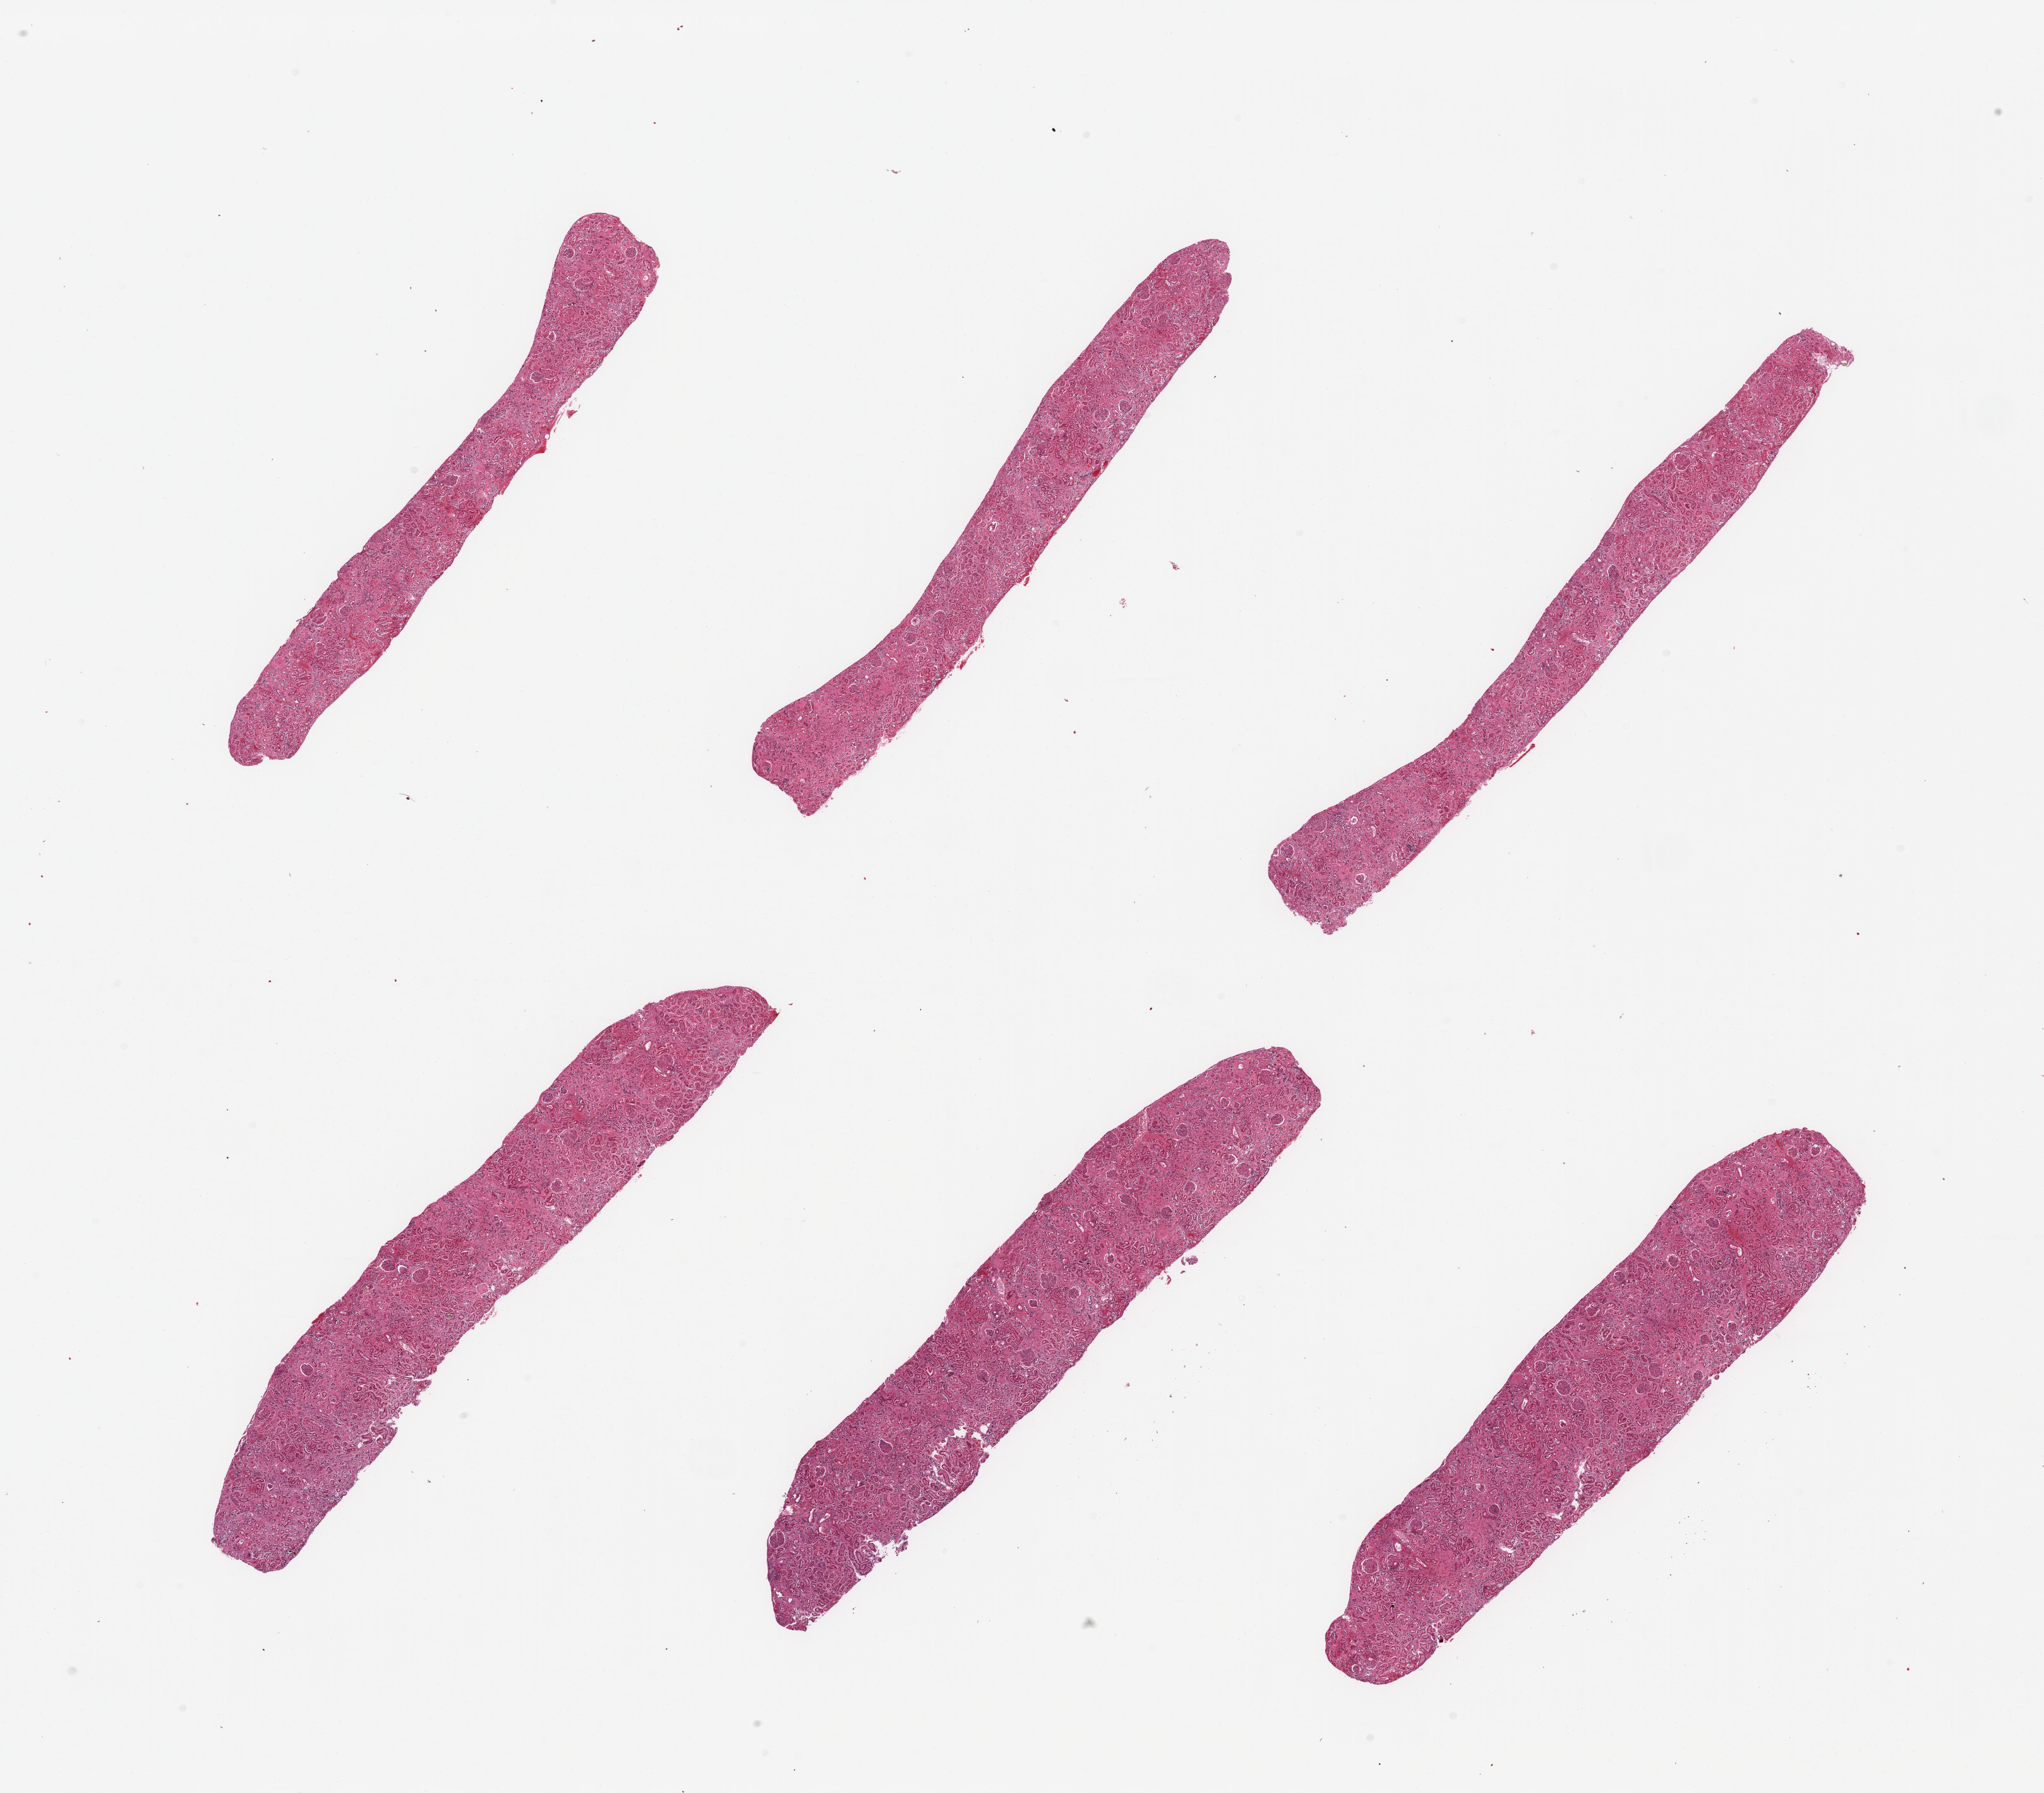
Hematoxylin and eosin (H&E) whole-slide image, low-resolution overview of the scanned area, about 25.6 x 22.4 mm (slide scanned at 20x), PAXgene-fixed, paraffin-embedded tissue, section of renal cortex (target tissue), tissue donor sample. Donor sex: female.
* reviewer comment on this tissue sample: 6 pieces; moderate interstitial fibrosis and arteriolar sclerosis